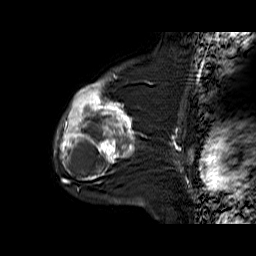
Breast MRI (dynamic contrast-enhanced), one sagittal slice; slice 44 of 60 in the series (ordered by position); dynamic contrast-enhanced series, time point 2 of 6 at this slice position (early post-contrast); 1.5 T; TE 6.3 ms, TR 32.9 ms; 4 mm slice thickness; 256 × 256 image matrix, field of view 200 × 200 mm. Female patient. Case-level facts recorded for this patient, not image findings: setting: breast cancer imaged before/during neoadjuvant chemotherapy; receptor status: triple-negative.
Outlined on this slice (semi-automatic segmentation, software-assisted and operator-edited):
- analysis volume of interest (the breast-tissue region the enhancement analysis was run in; not a lesion): bounding box <55,76,139,170> (left, top, right, bottom; pixels)
- tumour enhancement mask (voxels above the 100 % enhancement threshold inside the analysis volume of interest): <56,79,135,162>